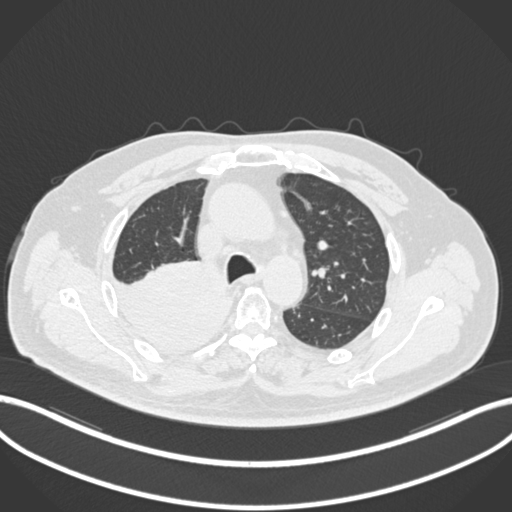
Chest CT, one axial slice; position 143 of 218 along the scan axis; reconstruction kernel B30f; 120 kVp; lung window (W 1500 / L -600 HU); 1 mm slice thickness; 512 × 512 image matrix, field of view 400 × 400 mm. Male patient, age 68 years. From the clinical record (not read from this slice): clinical TNM (as recorded): T2a N0 M0.
Annotated regions visible in this slice (rectangle marked by the reading radiologist):
- lung tumour (recorded histology: adenocarcinoma): box from (x=114, y=259) to (x=230, y=355) px